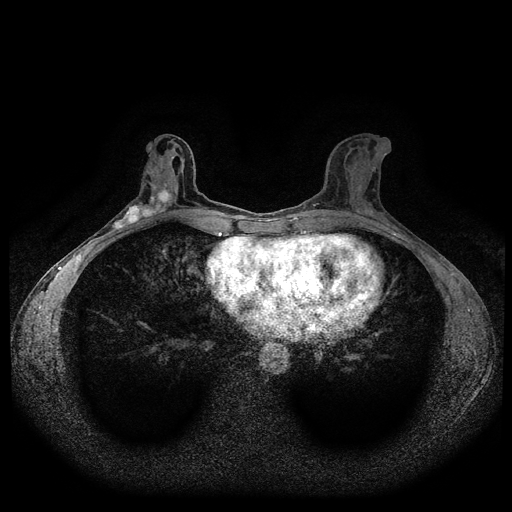
Breast MRI (dynamic contrast-enhanced, multi-phase), one axial slice. Slice 48 of 116 in the series (ordered by position). Dynamic contrast-enhanced series, time point 2 of 5 at this slice position (early post-contrast). 1.5 T. TE 2.6 ms, TR 5.3 ms. 2 mm slice thickness. 512 × 512 image matrix. Patient: female, 50 years.
Annotated regions visible in this slice (semi-automatic segmentation, software-assisted and operator-edited):
- breast lesion (labelled 'tumour' in the annotation; benign lesions carry a separate 'benign' label): bounding box <112,188,172,229> (left, top, right, bottom; pixels)